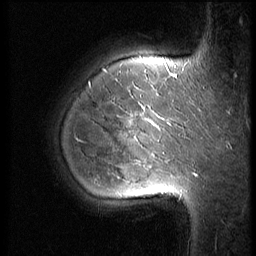
Breast MRI (dynamic contrast-enhanced), one sagittal slice; position 48 of 56 along the scan axis; 3 images stored at this slice position (order not interpretable as contrast timing); 1.5 T; TE 4.2 ms, TR 9 ms; 2.5 mm slice thickness; 256 × 256 image matrix, field of view 180 × 180 mm. Female patient, age 35 years. Case-level facts recorded for this patient, not image findings: setting: breast cancer imaged before/during neoadjuvant chemotherapy; receptor status: HR-positive, HER2-negative.
Outlined on this slice (semi-automatically segmented with operator editing):
- analysis volume of interest (the breast-tissue region the enhancement analysis was run in; not a lesion): bounding box <63,60,190,218> (left, top, right, bottom; pixels)
- tumour enhancement mask (voxels above the 140 % enhancement threshold inside the analysis volume of interest): <131,114,158,127>